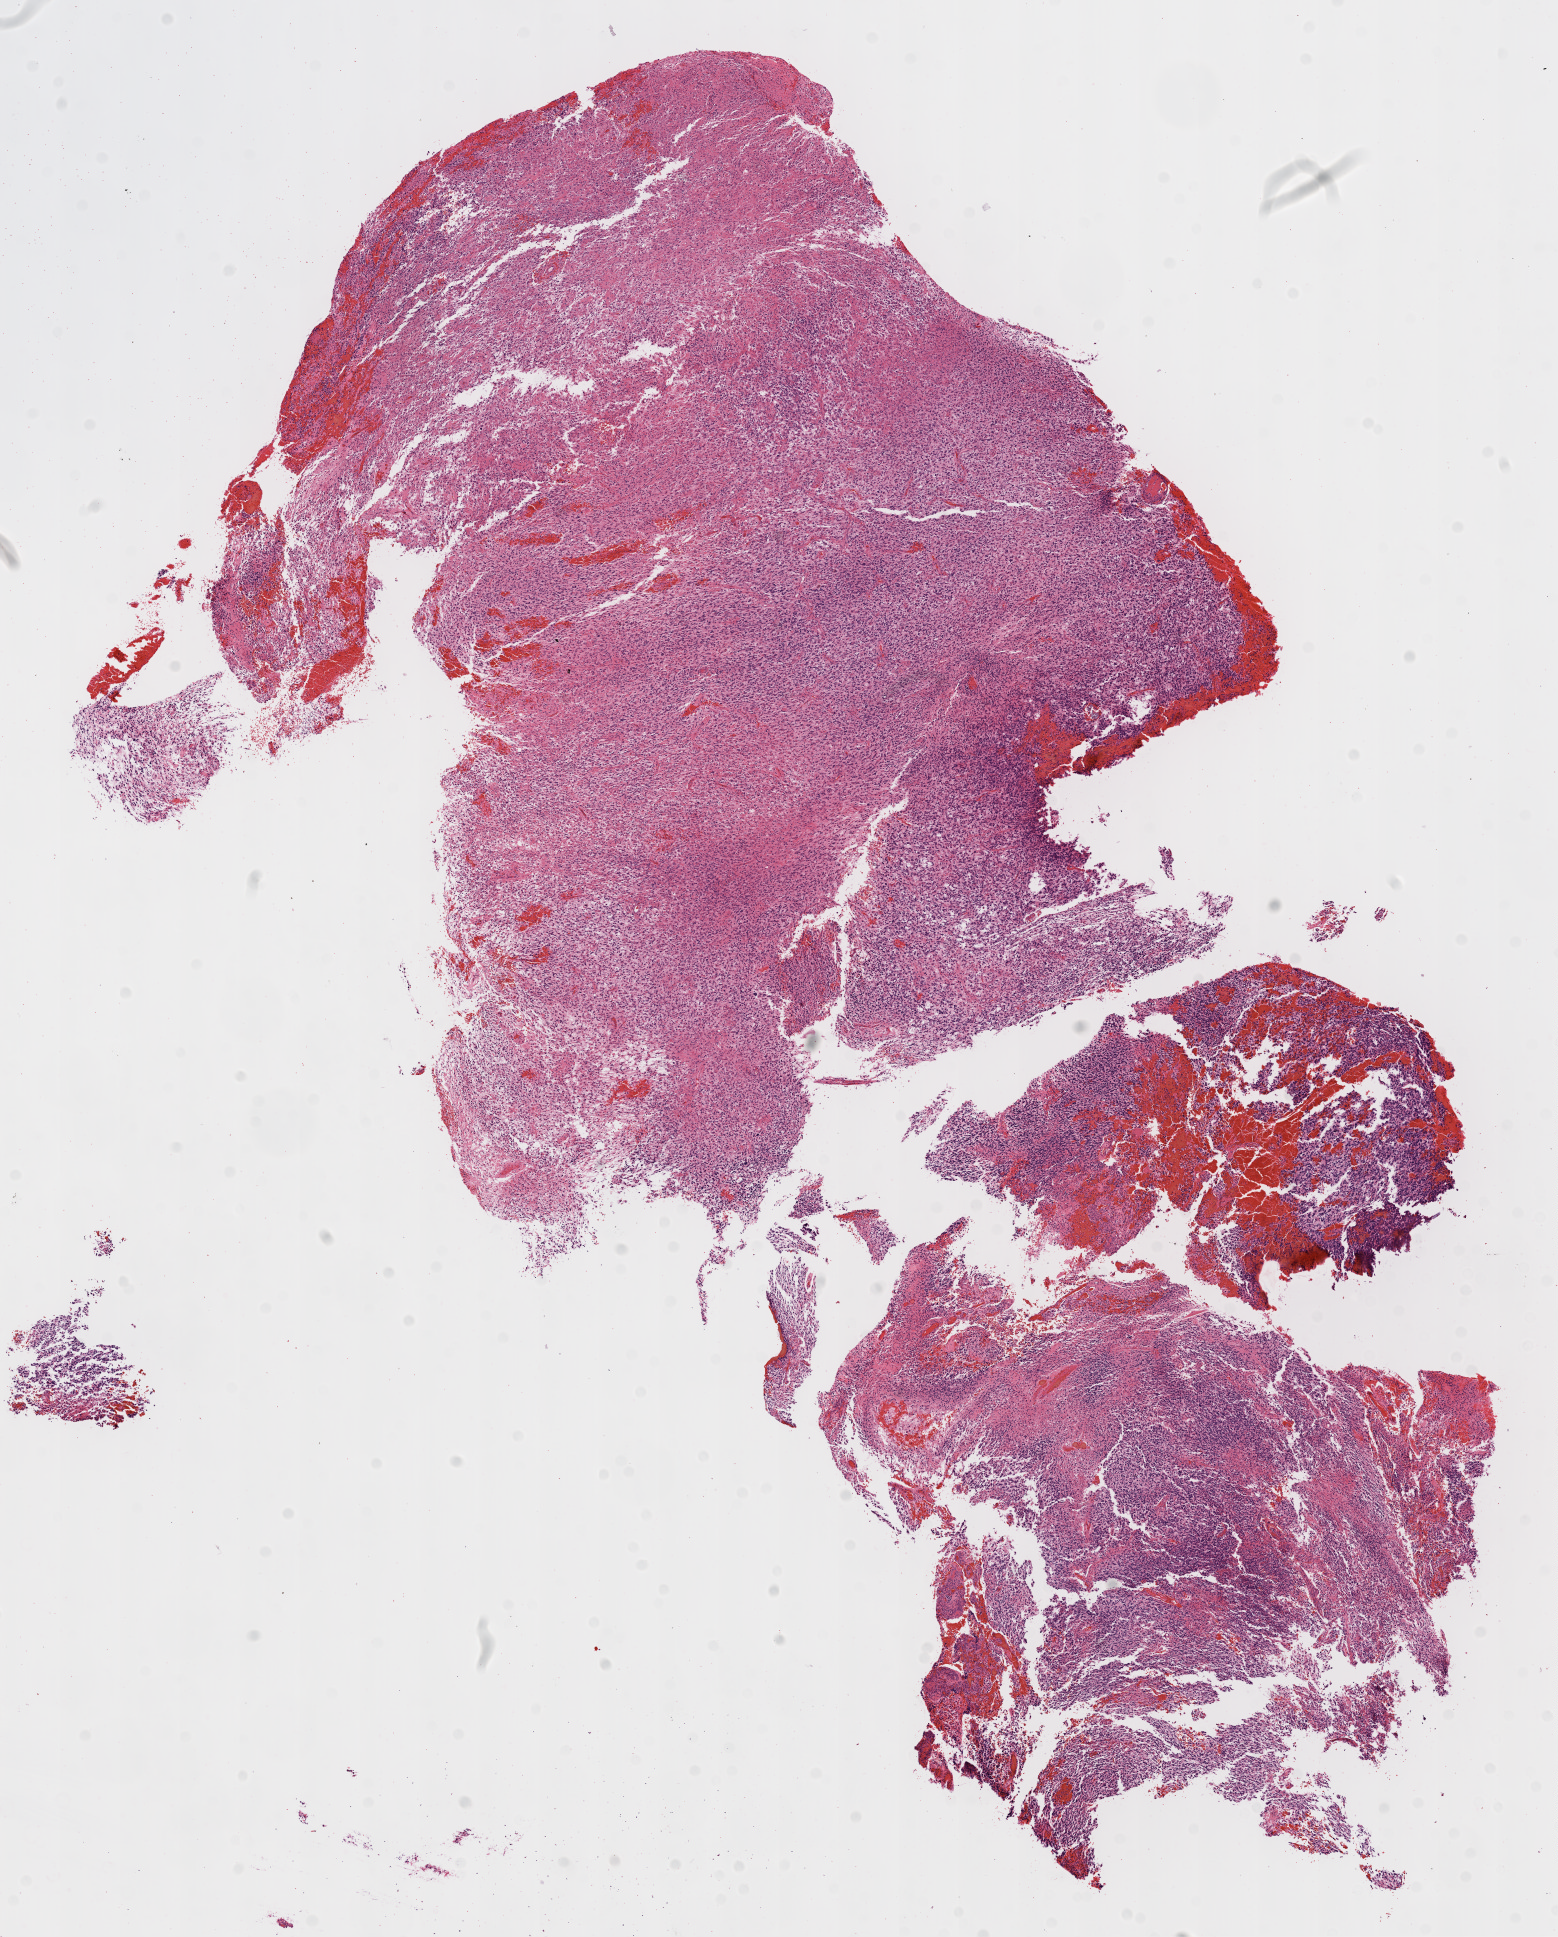
Hematoxylin and eosin (H&E) stained whole-slide image — low-resolution overview of the scanned area, about 12.6 x 15.6 mm (from a 20x scan); formalin-fixed paraffin-embedded (FFPE) diagnostic section; brain, primary tumour sample. Male, age 31 years at initial diagnosis.
Pathologic diagnosis: Glioblastoma.